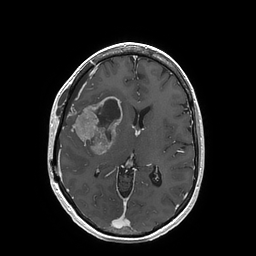
Brain MRI from a brain-tumour surgery series, one axial slice. Position 84 of 202 along the scan axis. T1-weighted post-contrast. 256 × 256 image matrix, field of view 250 × 250 mm. Case-level facts recorded for this patient, not image findings: histopathology: Glioblastoma; WHO grade: 4; IDH mutation: no; tumour location: Right Insular.
Annotated regions visible in this slice (expert manual segmentation):
- tumour: box from (x=74, y=97) to (x=122, y=155) px